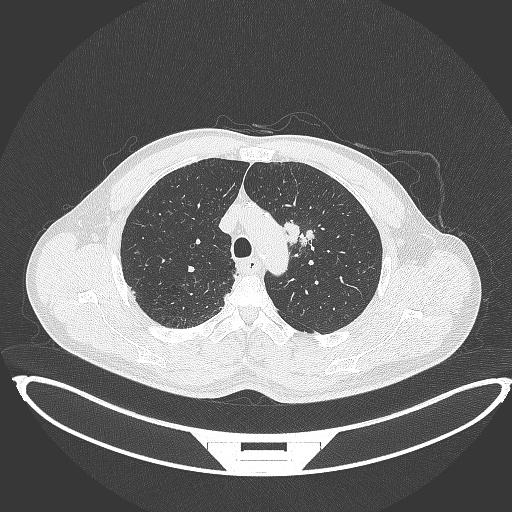
Chest CT, one axial slice. Position 332 of 395 along the scan axis. 120 kVp. Lung window (W 1500 / L -600 HU). 1 mm slice thickness. 512 × 512 image matrix, field of view 457 × 457 mm. Male patient, age 60 years. From the clinical record (not read from this slice): clinical TNM (as recorded): T2a N0 M0.
Annotated regions visible in this slice (rectangle marked by the reading radiologist):
- lung tumour (recorded histology: squamous cell carcinoma): box from (x=284, y=214) to (x=315, y=250) px